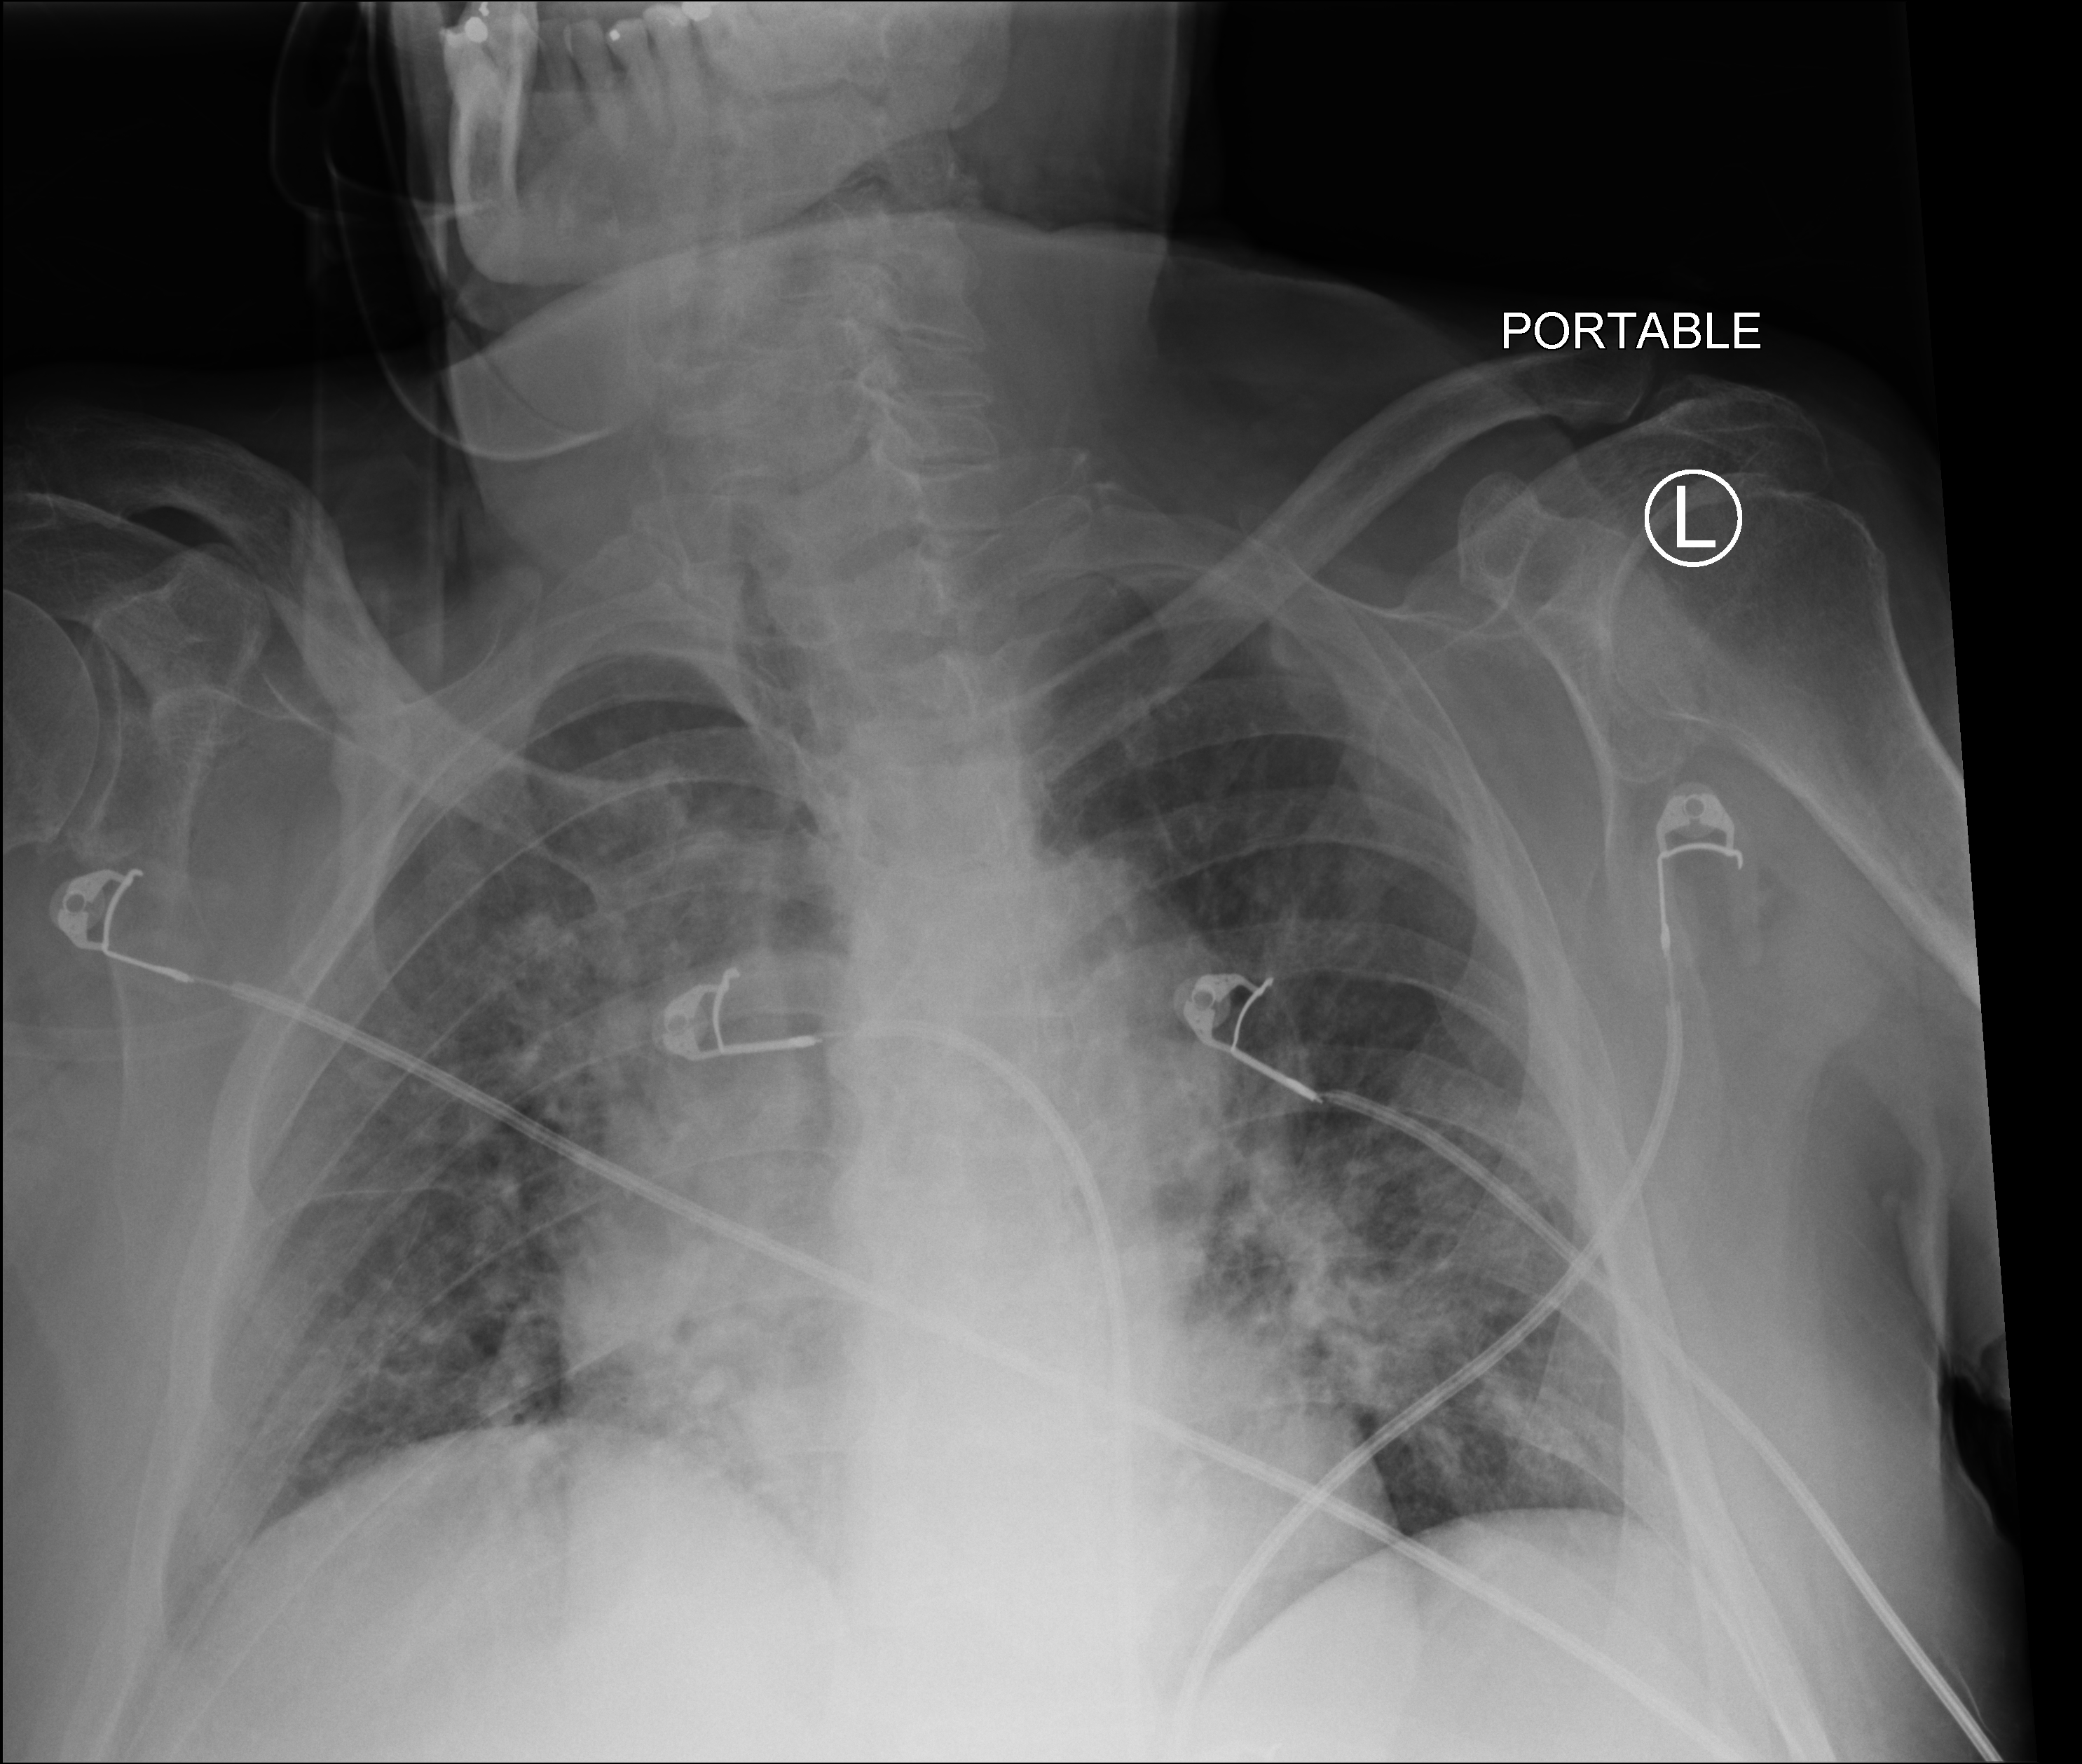
Portable chest radiograph; anteroposterior (AP) projection. Male patient hospitalised with COVID-19, age 75–90 years.
From the hospital-stay record, not from the radiograph (when in the stay this image was taken is not recorded):
- length of hospital stay: 5 days
- mechanically ventilated during this hospital stay: no